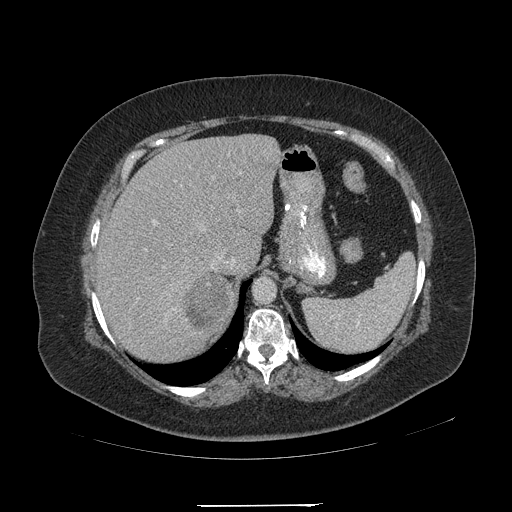
Contrast-enhanced abdominal CT, one axial slice. Position 161 of 217 along the scan axis. 120 kVp. Intravenous contrast given. Soft-tissue window (W 400 / L 40 HU). 1.25 mm slice thickness. 512 × 512 image matrix, field of view 453 × 453 mm. Female patient, age 55 years. Case-level facts recorded for this patient, not image findings: diagnosis: adrenocortical carcinoma; tumour side: right adrenal; tumour size at pathology: 11 cm; Ki-67 index: 20 %; stage (as recorded): 2.
Outlined on this slice (semi-automatic segmentation, software-assisted and operator-edited):
- mass: bounding box <183,275,232,331> (left, top, right, bottom; pixels)